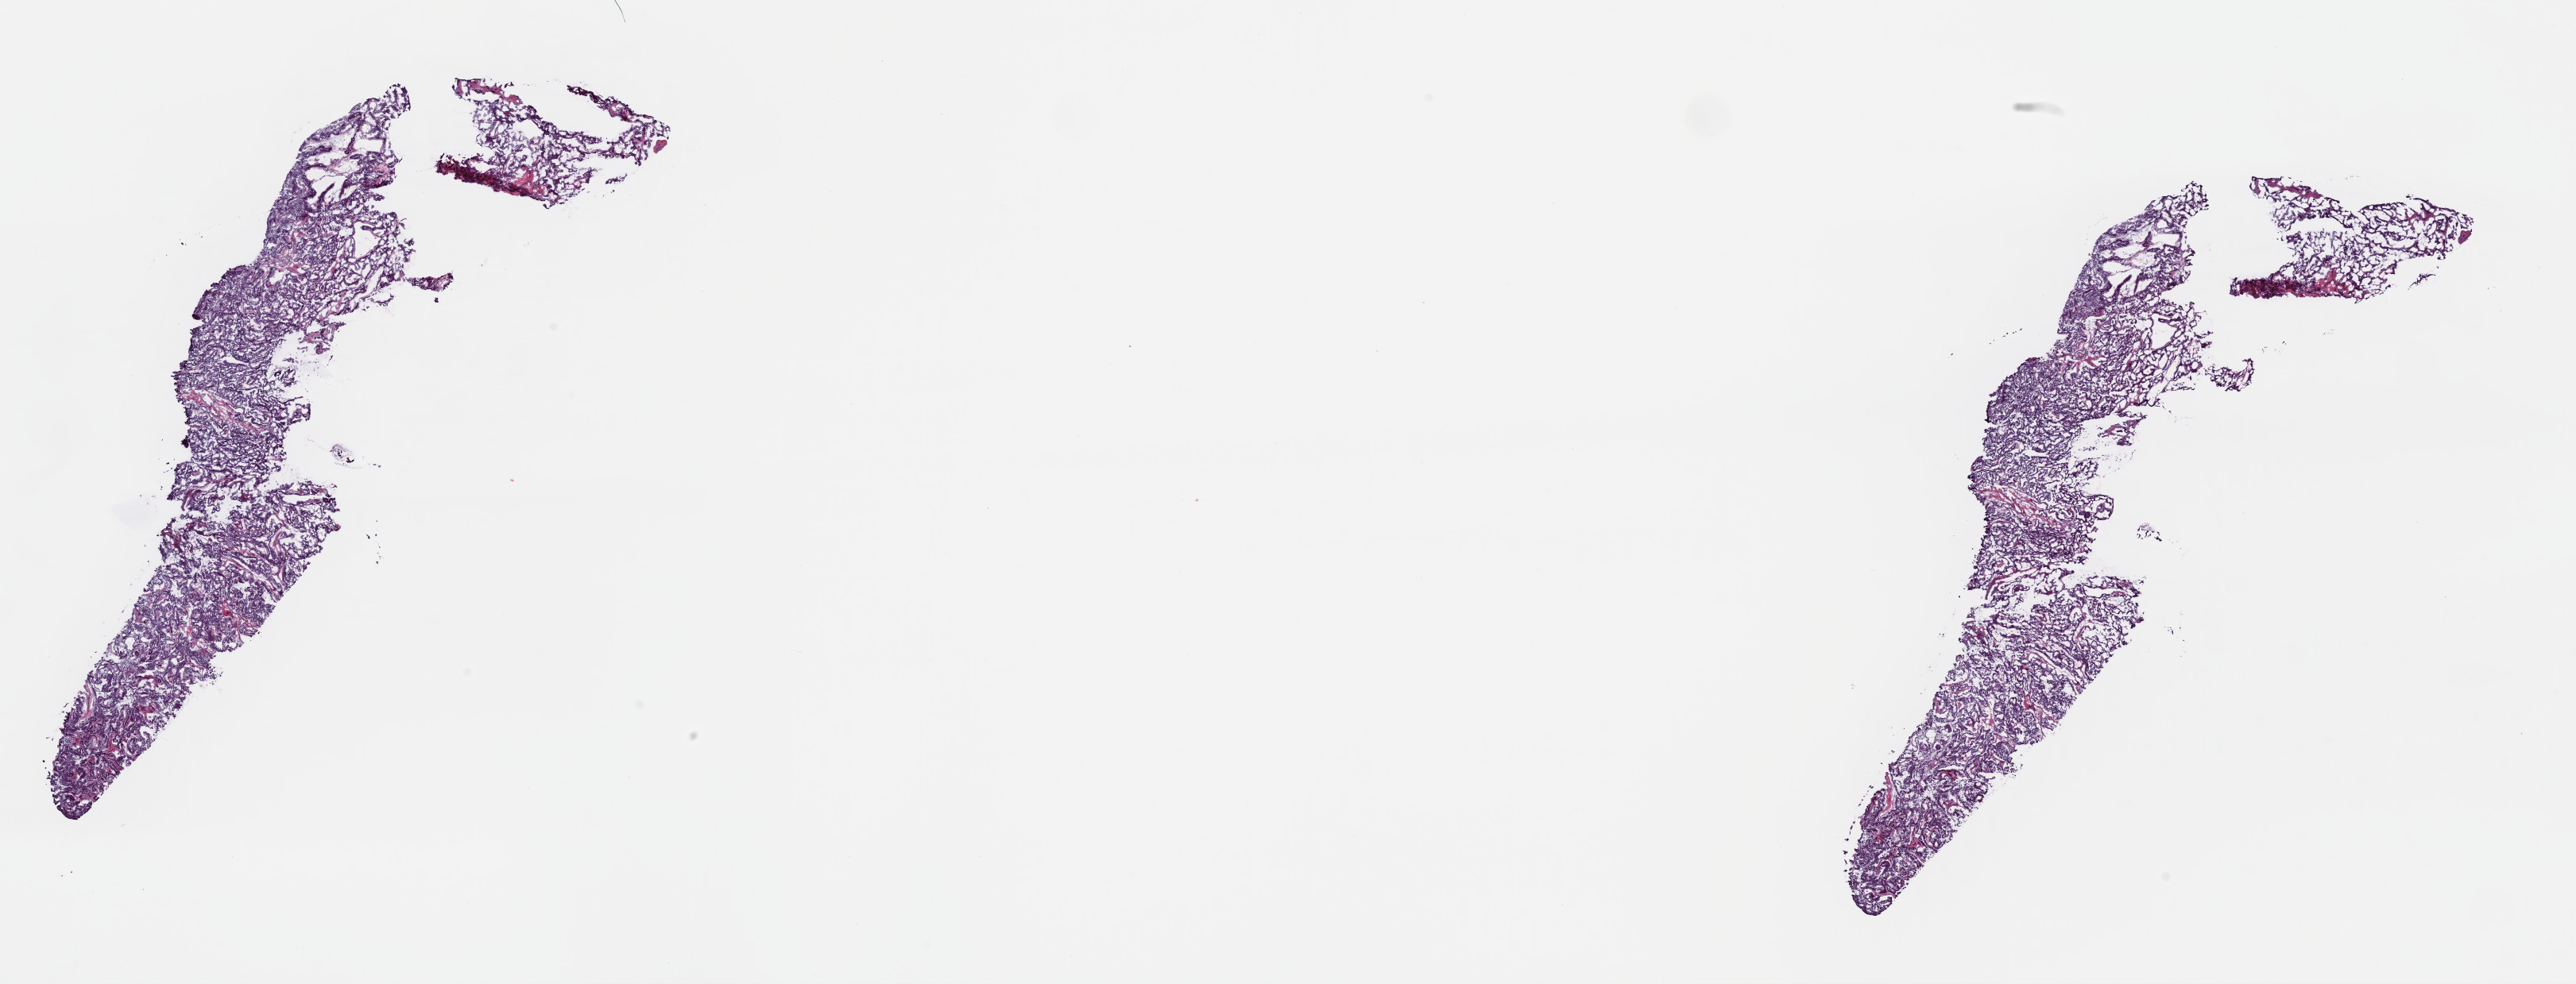
Hematoxylin and eosin (H&E) stained whole-slide image, whole scanned area (about 25.6 x 9.8 mm, acquisition: 40x scan) shown as a low-resolution overview; frozen section; primary tumour sample from the thyroid. Female, age 37 years at initial diagnosis. Slide review estimates, as recorded: tumour cells 90%, tumour nuclei 100%, normal cells 0%, stromal cells 10%, necrosis 0%. Inflammatory infiltration, as recorded: lymphocyte infiltration 0%, monocyte infiltration 1%, neutrophil infiltration 0%.
• lymph nodes positive (case pathology): 1 of 1 examined
• TNM: T3 N1 M0
• diagnosis: Papillary adenocarcinoma, NOS (thyroid gland)
• AJCC pathologic stage: I (6th edition)